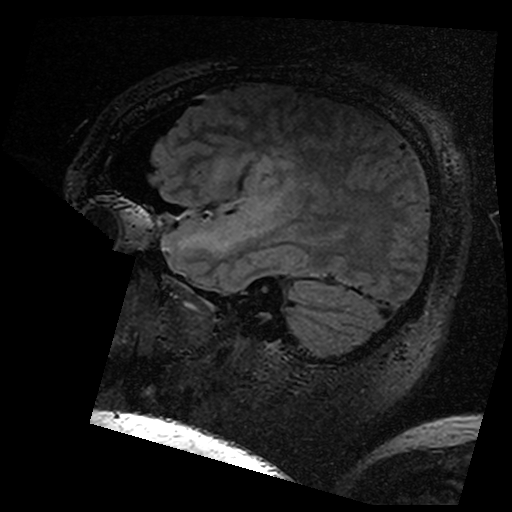
Brain MRI from a brain-tumour surgery series, one sagittal slice; position 127 of 176 along the scan axis; T2 FLAIR; 1 mm slice thickness; 512 × 512 image matrix, field of view 250 × 250 mm. From the clinical record (not read from this slice): histopathology: Astrocytoma; WHO grade: 3; IDH mutation: yes.
Annotated regions visible in this slice (expert manual segmentation):
- residual tumour: box from (x=219, y=156) to (x=290, y=184) px